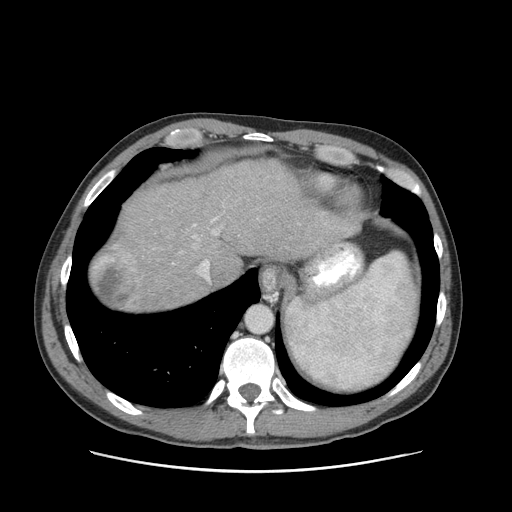
Contrast-enhanced abdominal CT (liver protocol), one axial slice; slice 80 of 93 in the series (ordered by position); reconstruction kernel STANDARD; 120 kVp; soft-tissue window (W 400 / L 40 HU); 2.5 mm slice thickness; 512 × 512 image matrix, field of view 380 × 380 mm. Case-level facts recorded for this patient, not image findings: diagnosis: hepatocellular carcinoma (patient treated with transarterial chemoembolisation; whether this scan precedes or follows treatment is not stated here); TNM stage (as recorded): Stage-II; Child-Pugh class: A; tumour differentiation: moderately differentiated; tumour nodularity: multinodular.
Annotated regions visible in this slice (semi-automatically segmented with operator editing):
- abdominal aorta: bounding box [x1, y1, x2, y2] px = [245, 305, 273, 332]
- liver parenchyma outside the tumour (the mass and vessels are separate outlines, so this box may not span the whole liver): [90, 160, 357, 310]
- mass: [93, 245, 140, 308]
- liver vessels: [193, 218, 217, 280]